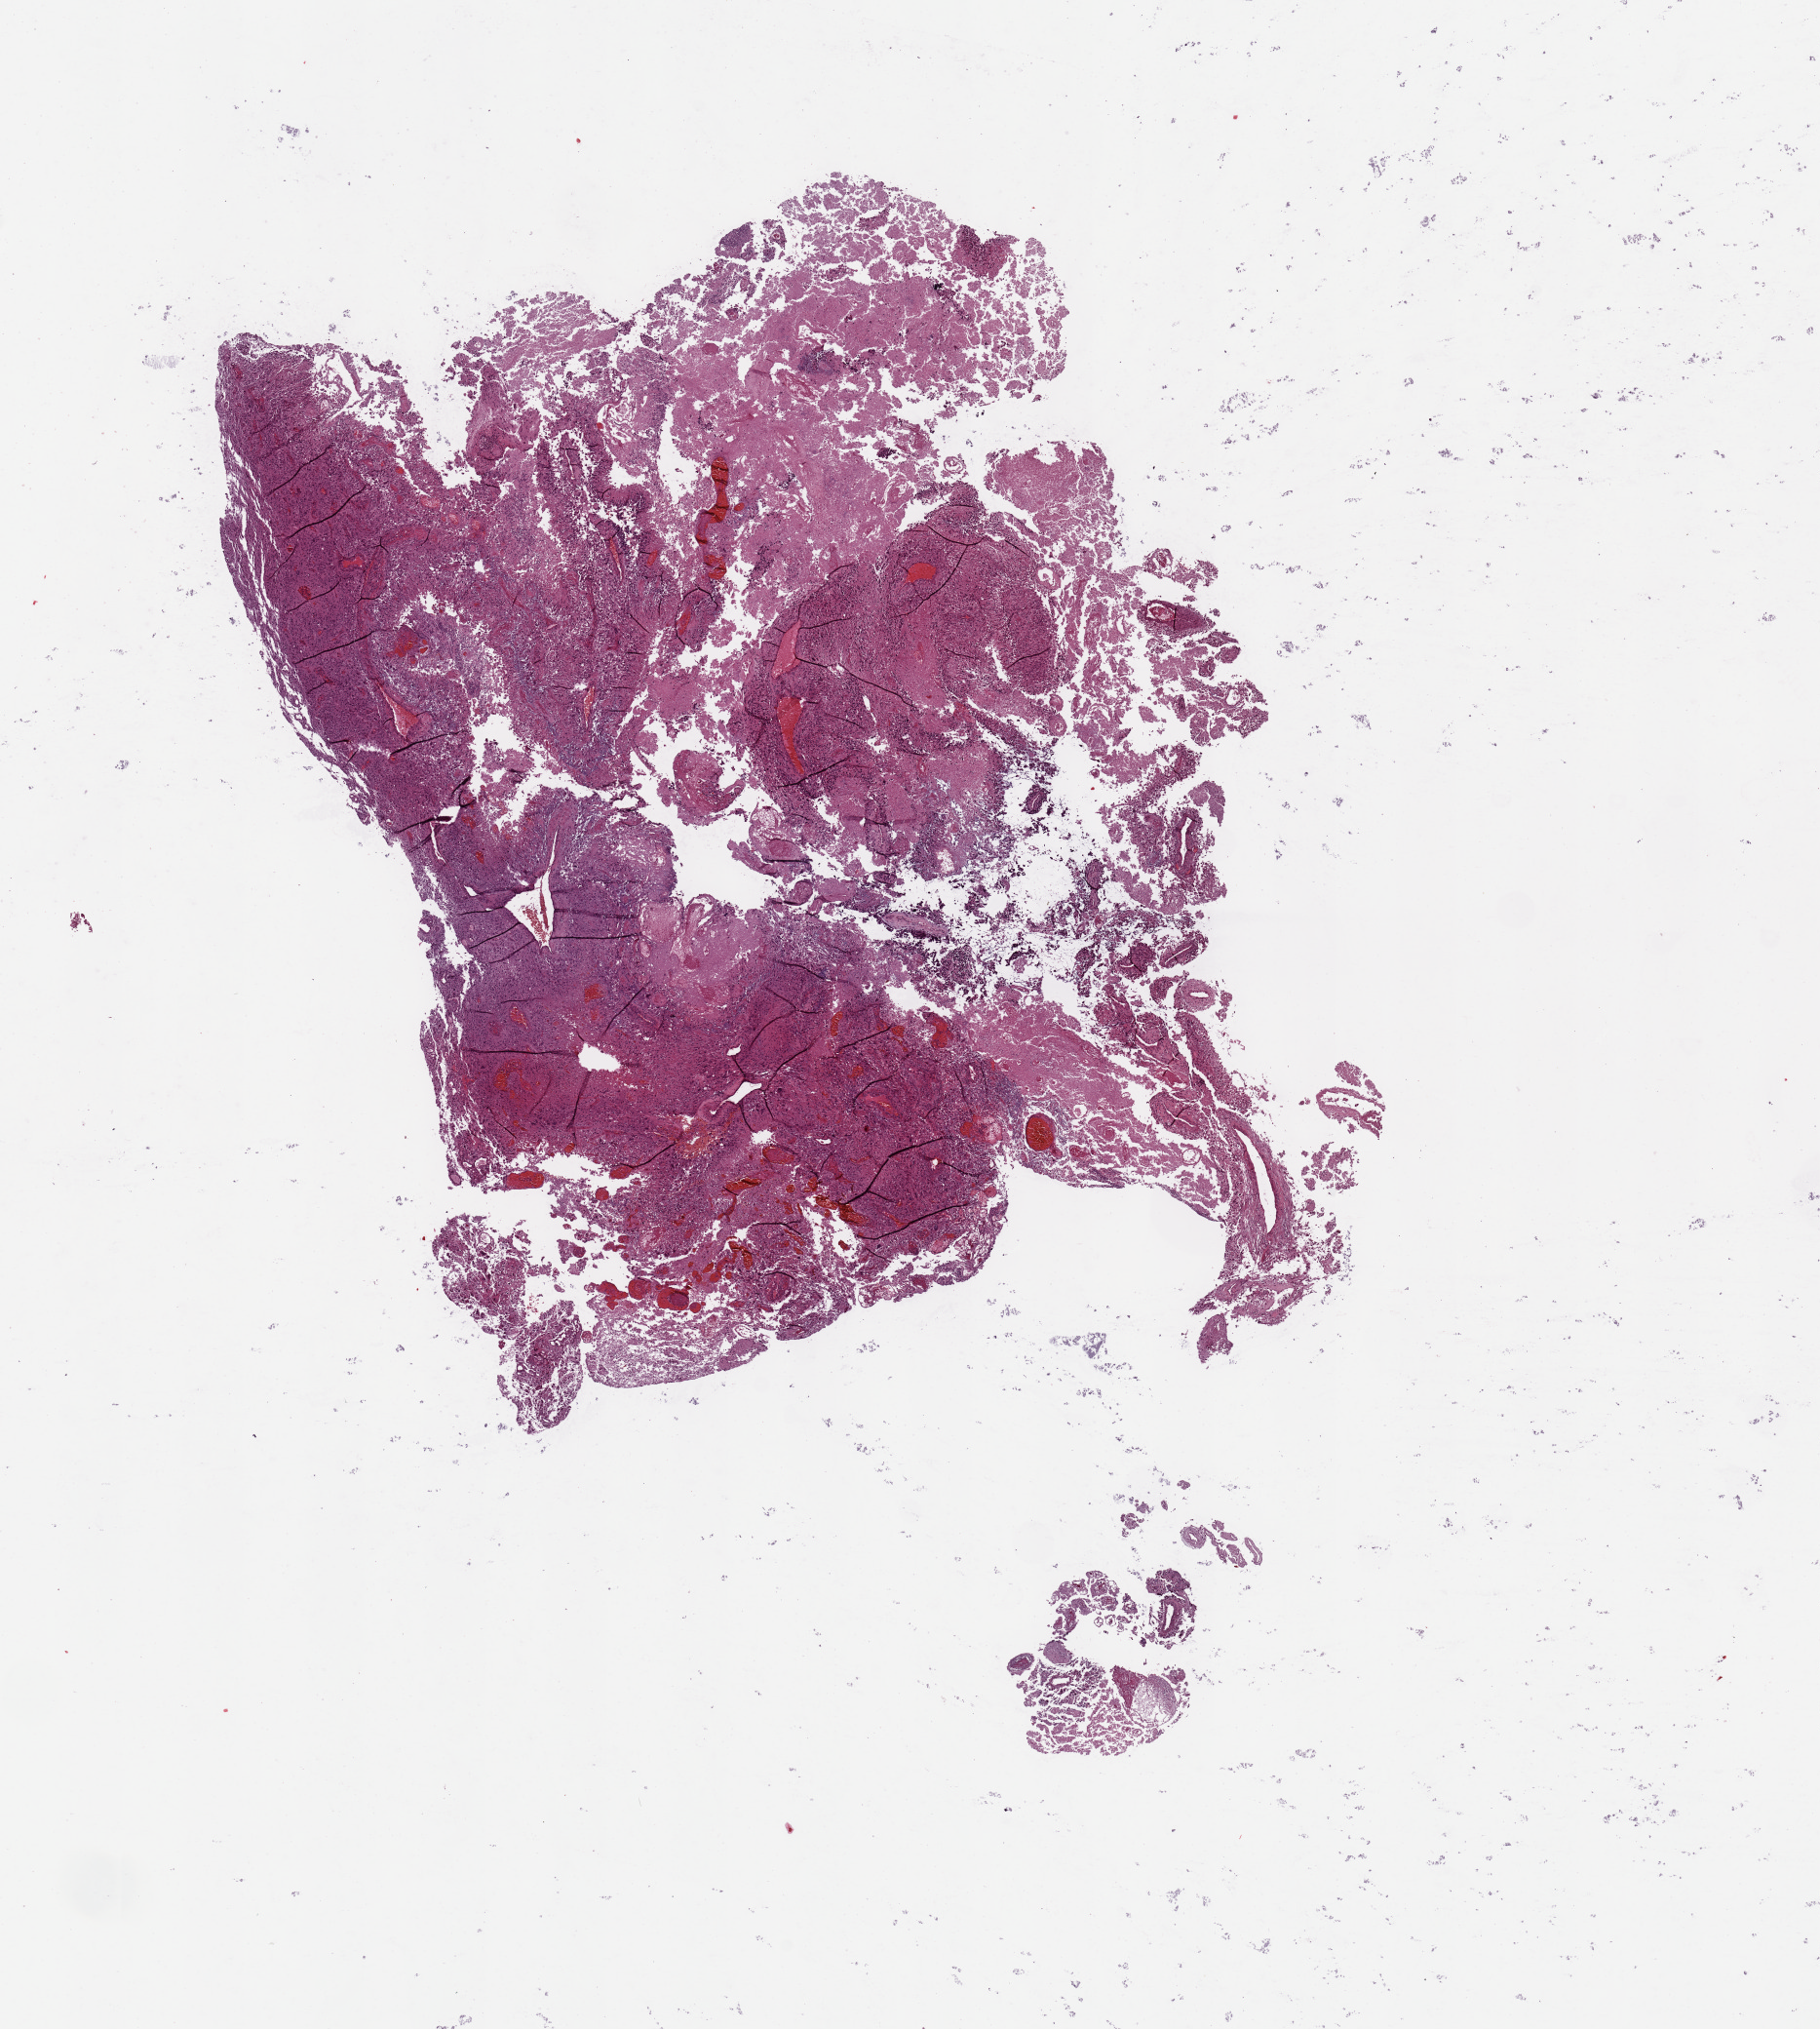
Digitized H&E-stained tissue section (whole slide), shown as a low-resolution overview of the whole scanned area (about 14.8 x 16.5 mm); brain, tumour tissue. Patient: male, age 60 years.
Histologic diagnosis: Glioblastoma.